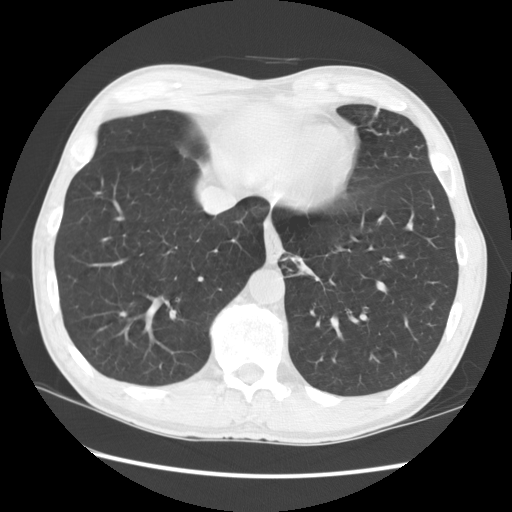
Low-dose screening chest CT, one axial slice; slice 34 of 141 in the series (ordered by position); reconstruction kernel STANDARD; lung window (W 1500 / L -600 HU); 512 × 512 image matrix, field of view 360 × 360 mm.
Outlined on this slice (outlined manually by an expert reader):
- lesion 1 (tumor, lower lobe of left lung): box from (x=375, y=108) to (x=378, y=116) px